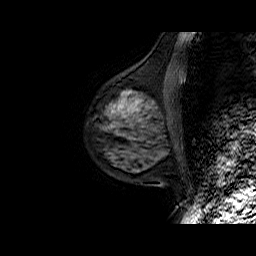
Breast MRI (dynamic contrast-enhanced), one sagittal slice; dynamic contrast-enhanced series, time point 2 of 6 at this slice position (early post-contrast); 1.5 T; TE 6.5 ms, TR 32.9 ms; 4 mm slice thickness; 256 × 256 image matrix, field of view 200 × 200 mm. Female patient. From the clinical record (not read from this slice): setting: breast cancer imaged before/during neoadjuvant chemotherapy; receptor status: HR-positive, HER2-negative.
Structures marked on this image (semi-automatic segmentation, software-assisted and operator-edited):
- analysis volume of interest (the breast-tissue region the enhancement analysis was run in; not a lesion): box from (x=89, y=75) to (x=178, y=149) px
- tumour enhancement mask (voxels above the 100 % enhancement threshold inside the analysis volume of interest): (x=111, y=92)–(x=130, y=113)